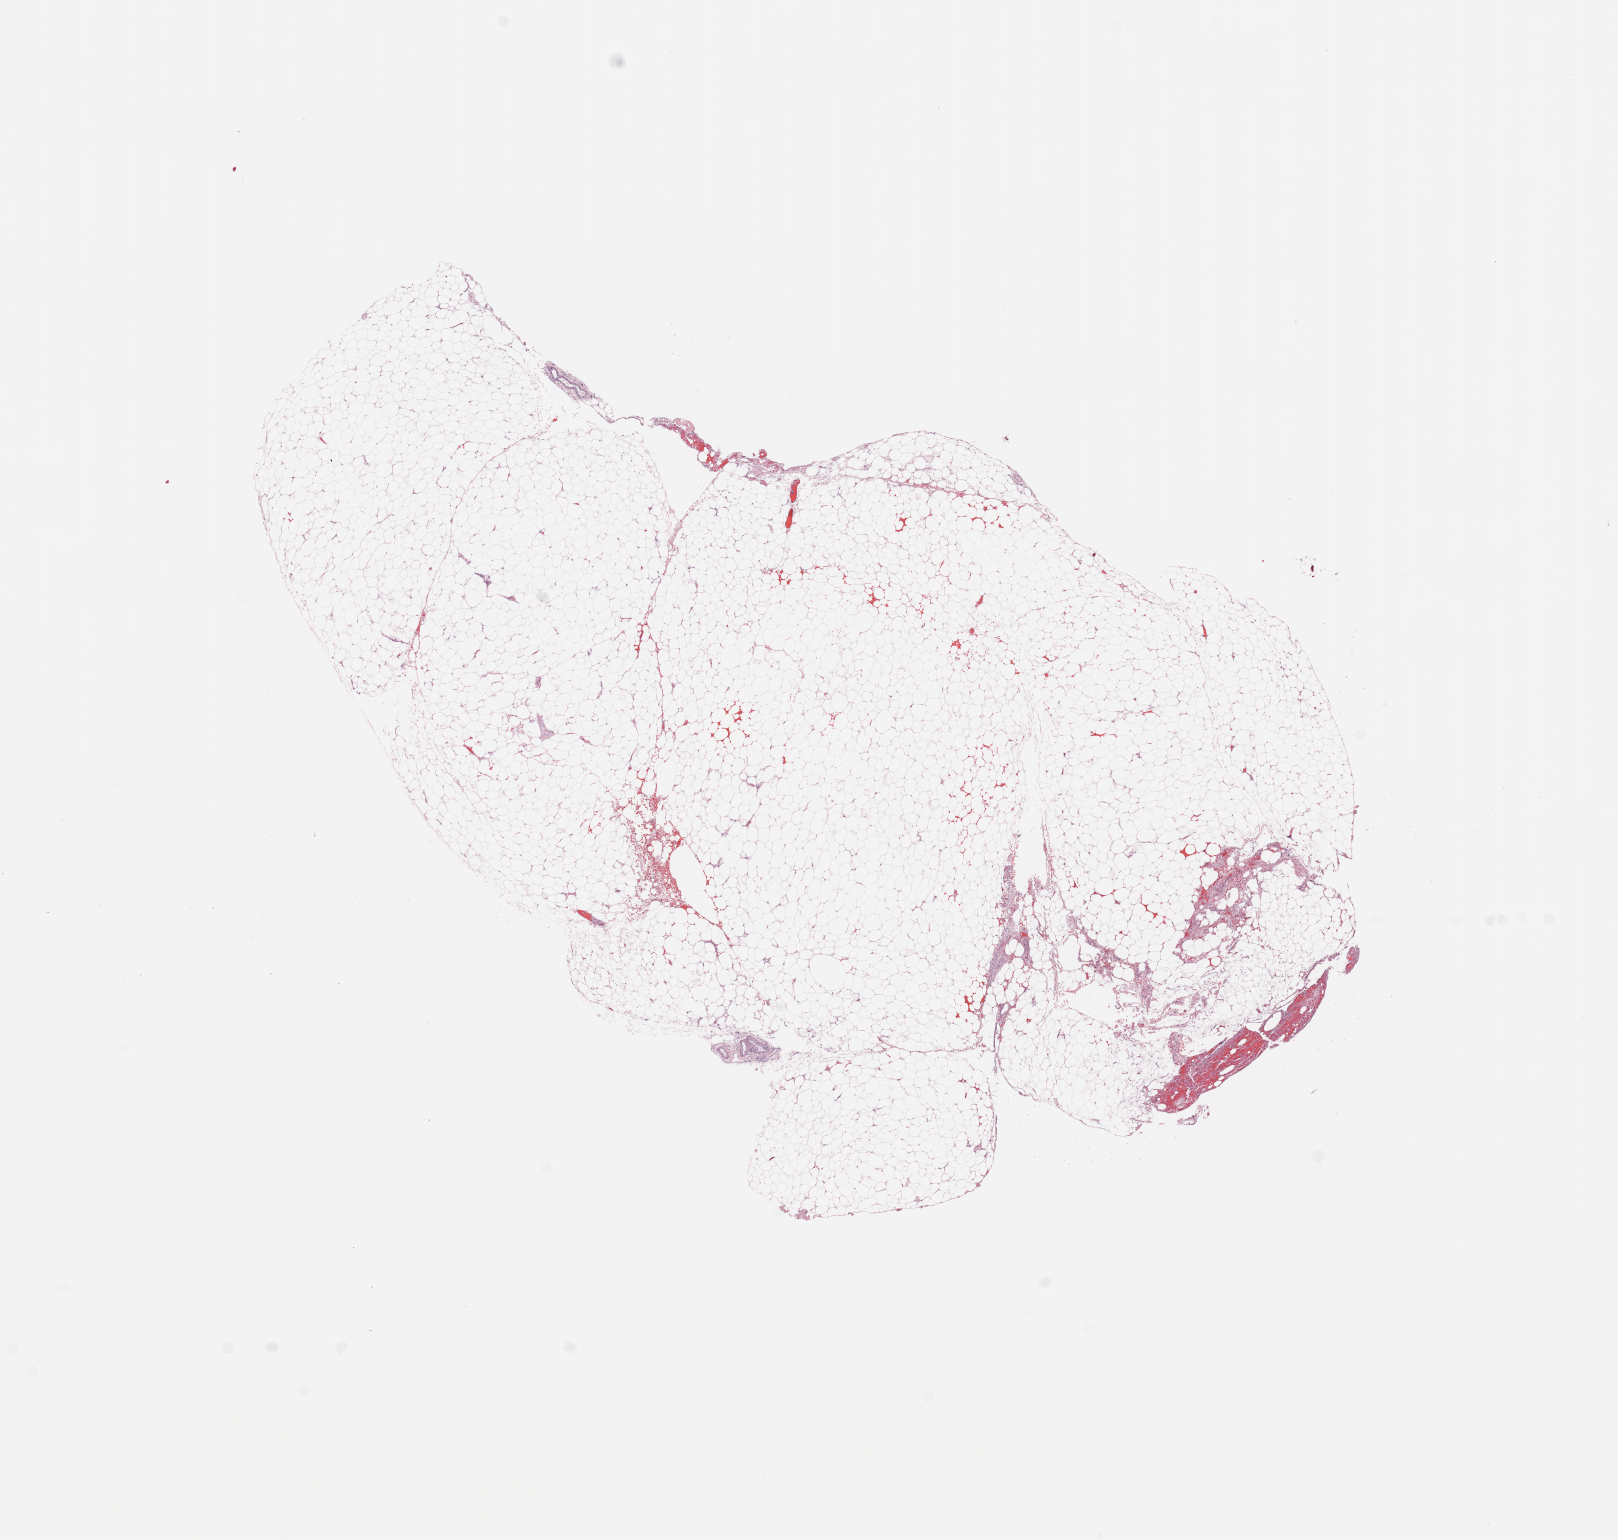
H&E whole-slide image — a low-resolution overview of the entire scanned area, about 12.8 x 12.2 mm (acquisition: 20x scan); kidney, normal (non-tumour) tissue. Patient: female, age 63 years.
• this section: normal (non-tumour) tissue from the same patient
• patient diagnosis: Renal cell carcinoma, NOS